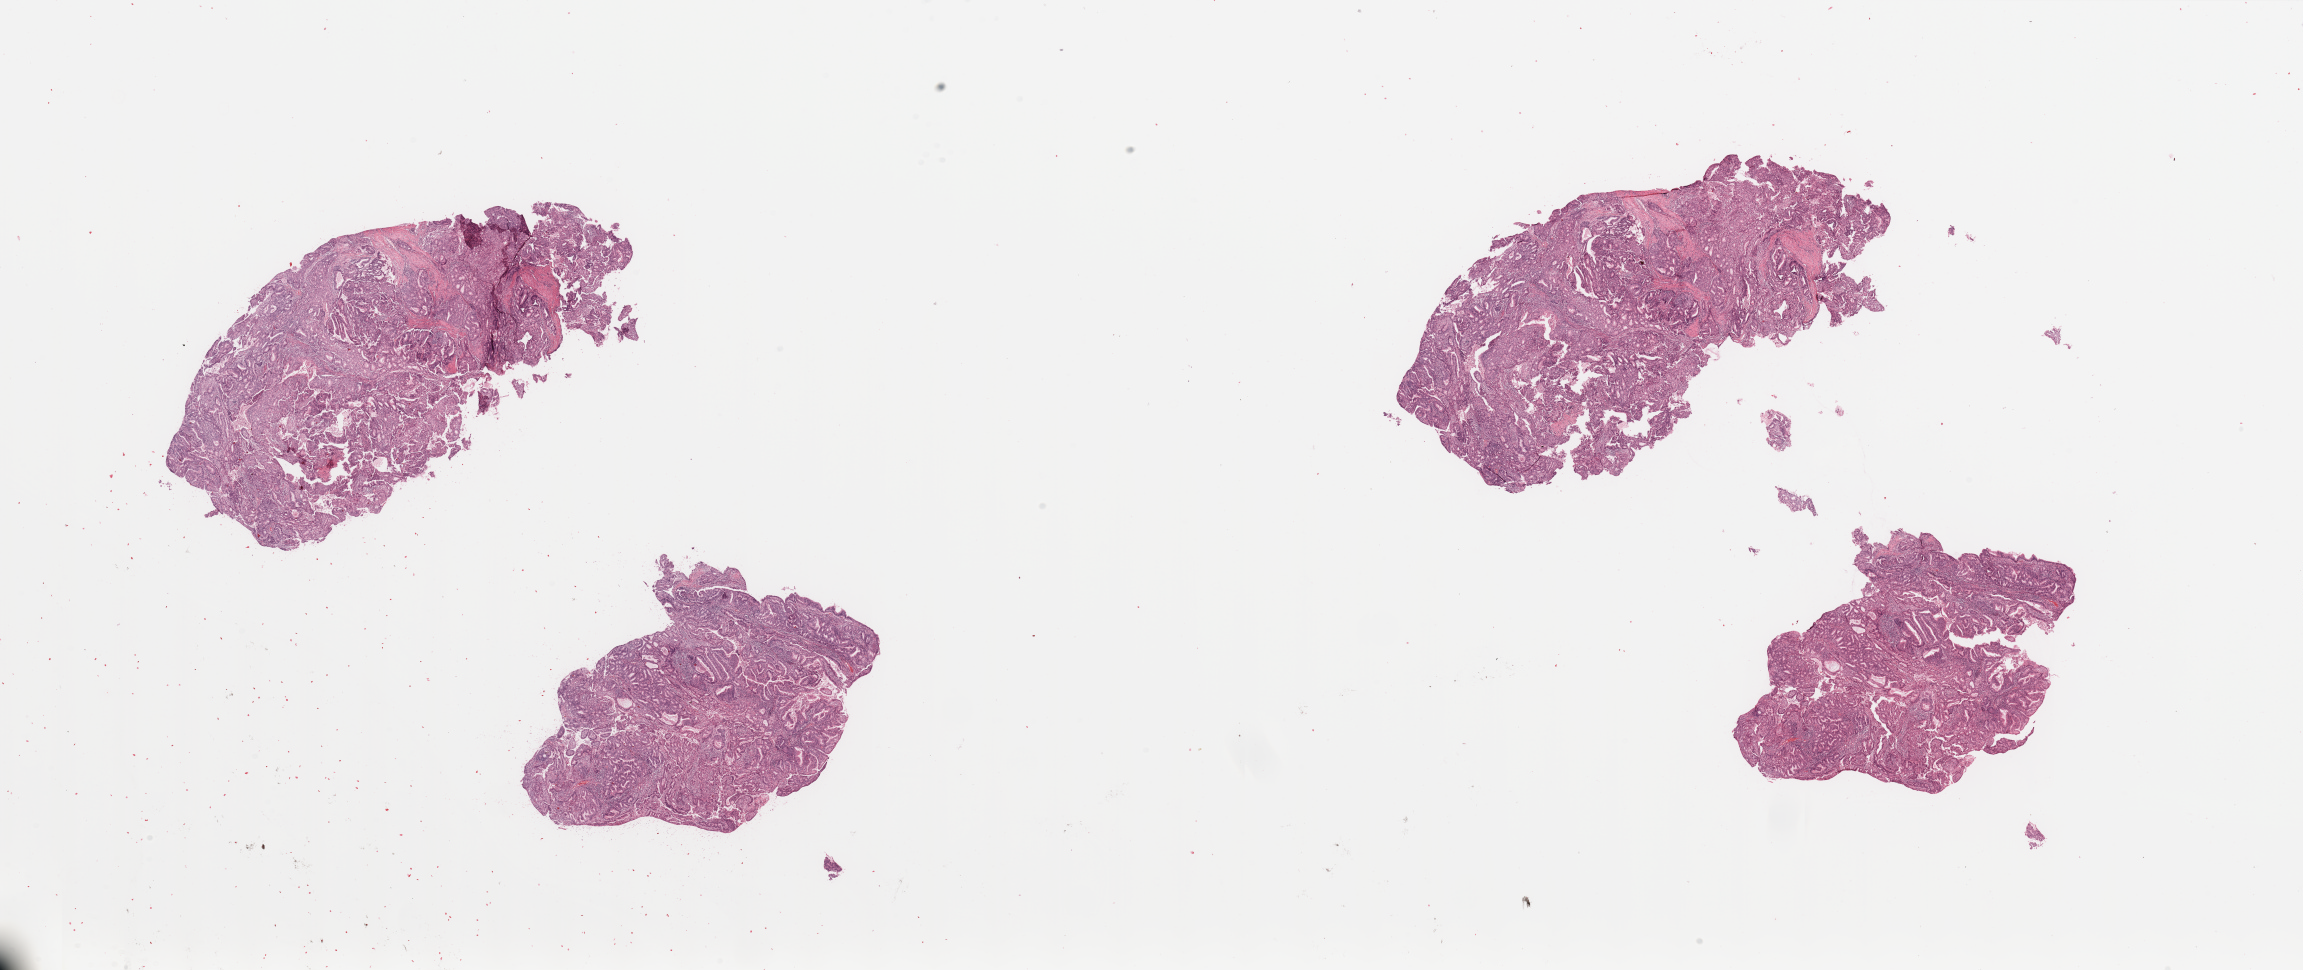
Whole-slide histology image, H&E, whole scanned area (about 36.4 x 15.3 mm) shown as a low-resolution overview; tumour tissue sample, sampled site: uterus. Female, 51 y/o. Histologic grade: G1 (well differentiated). Composition of this section per pathologist review: tumour nuclei 90%, necrosis 5%.
- diagnosis: Endometrioid adenocarcinoma, NOS
- AJCC pathologic stage: I